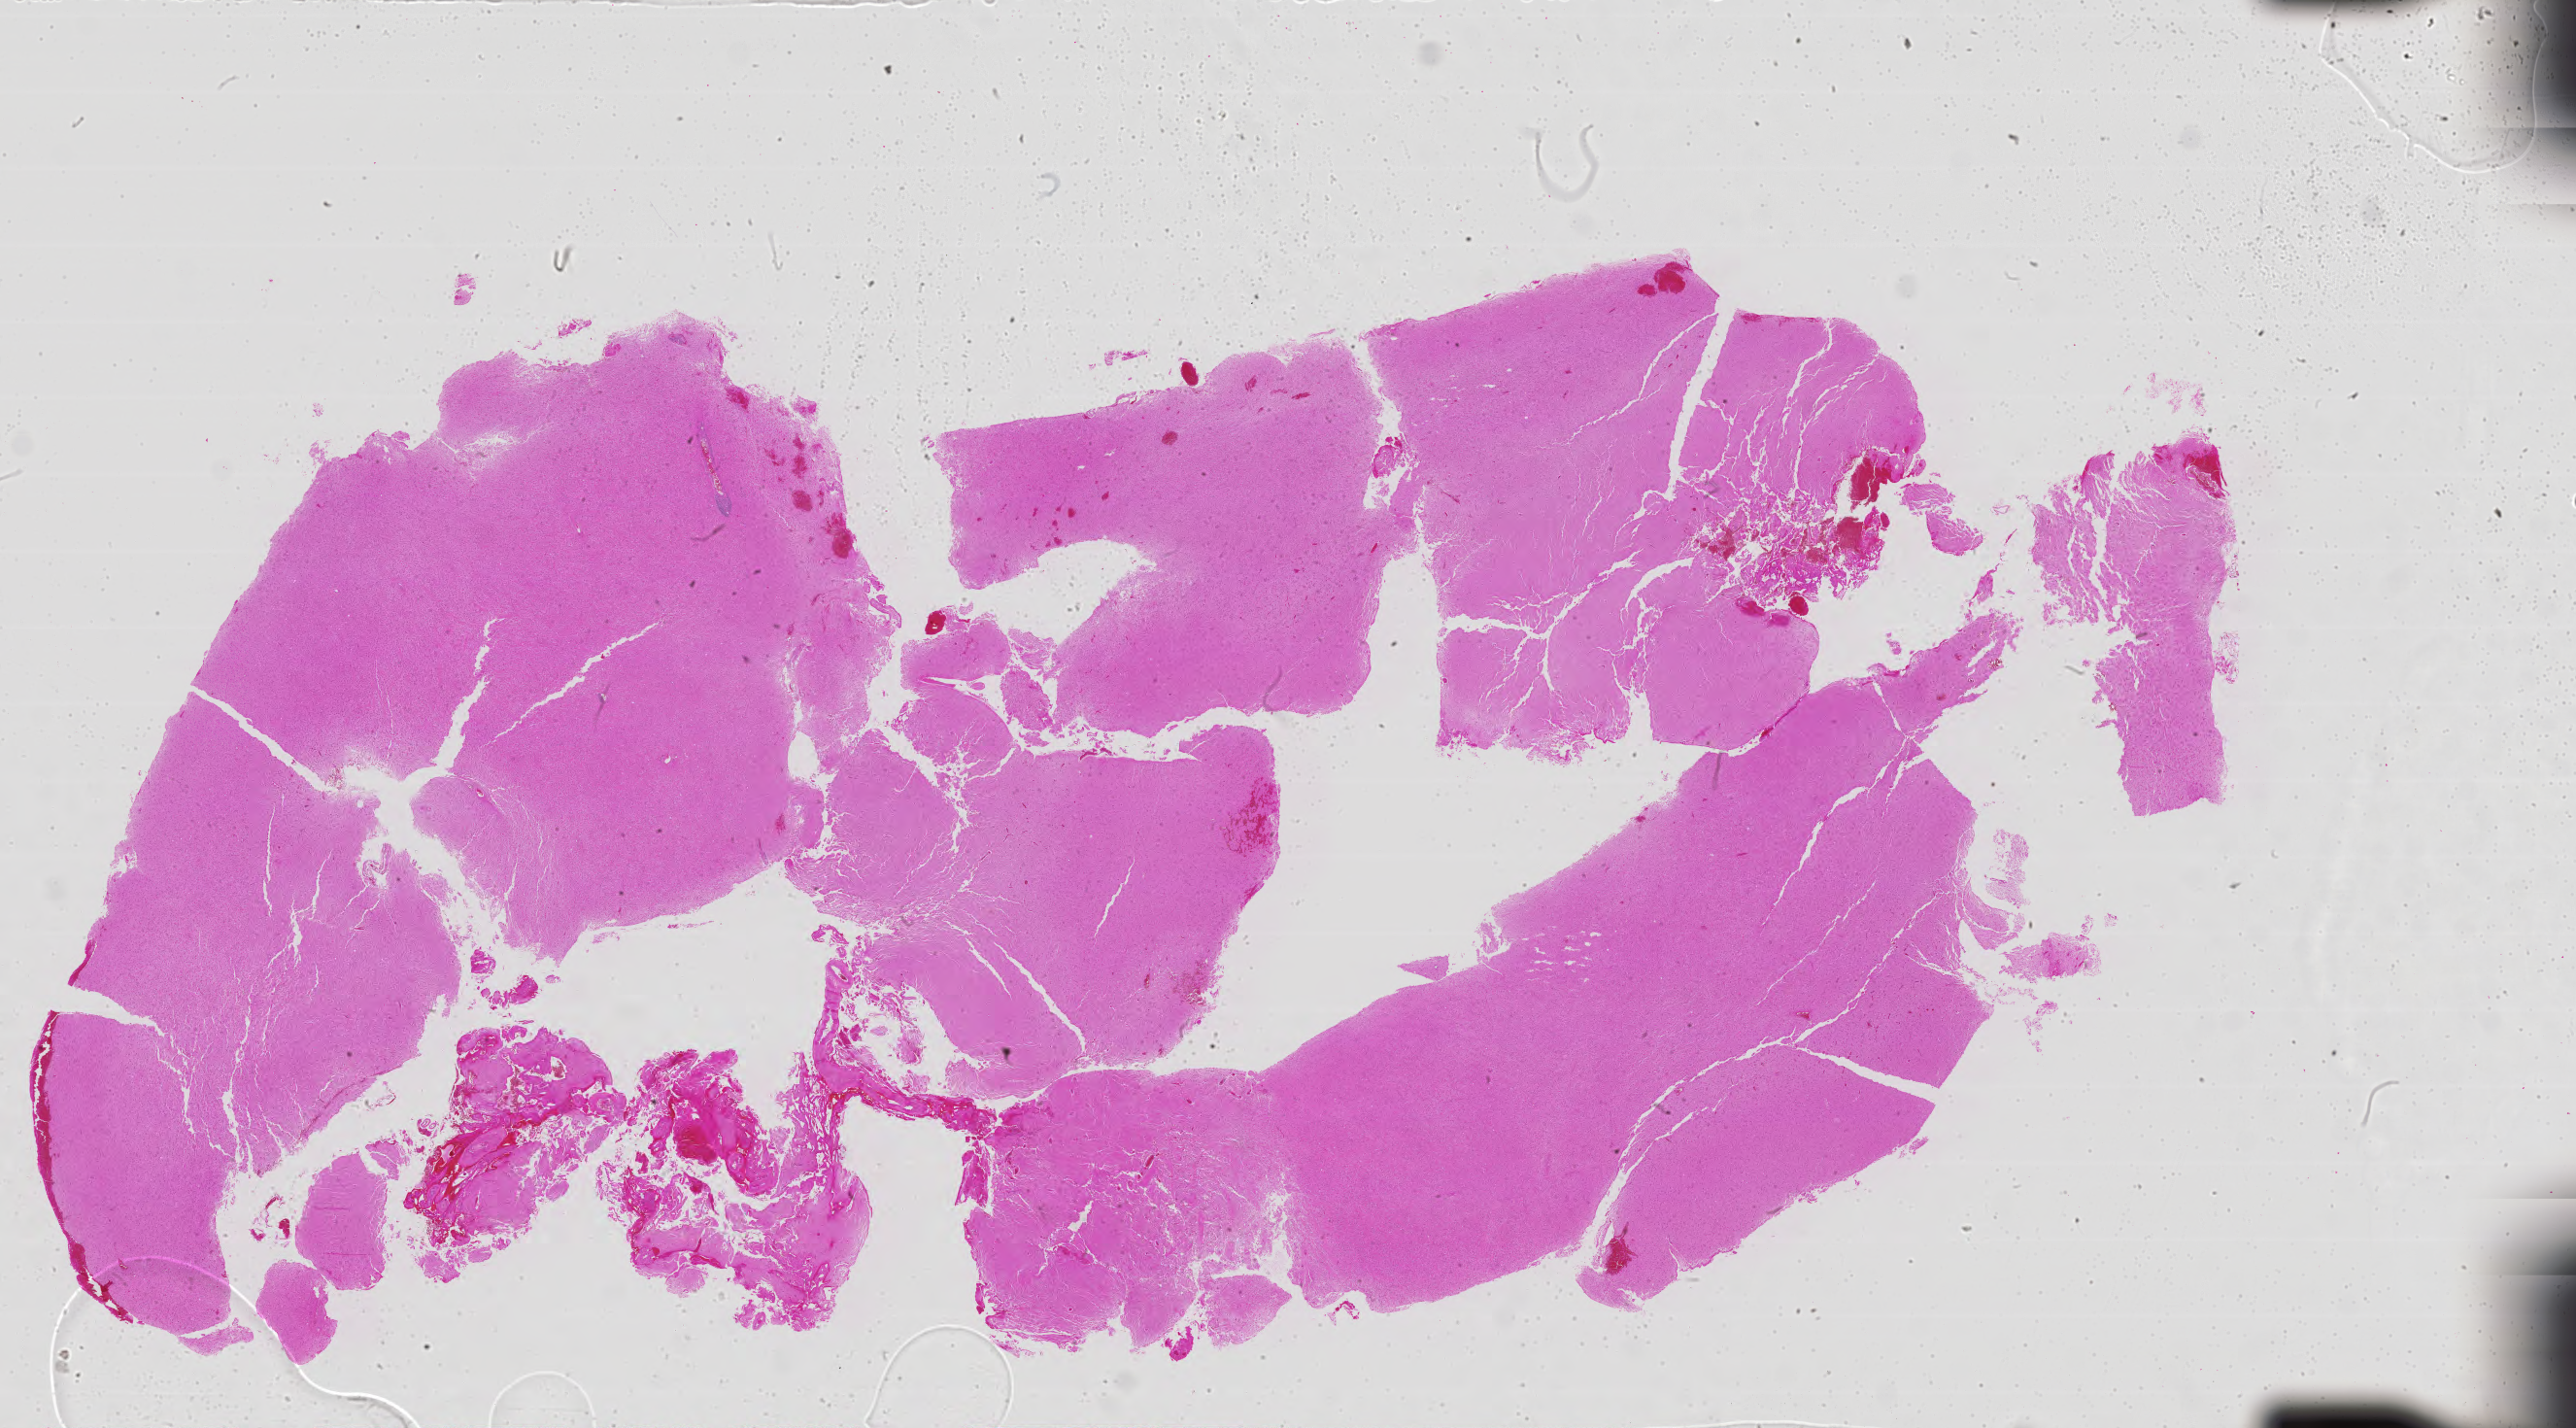
Whole-slide histology image, H&E-stained, shown as a low-resolution overview of the whole scanned area (about 42.4 x 23.5 mm); formalin-fixed paraffin-embedded (FFPE) diagnostic section; brain, primary tumour sample. Patient: male, age at initial diagnosis 52 years. Histologic grade: G3 (poorly differentiated).
* laterality: left
* histologic diagnosis: Astrocytoma, anaplastic (cerebrum)